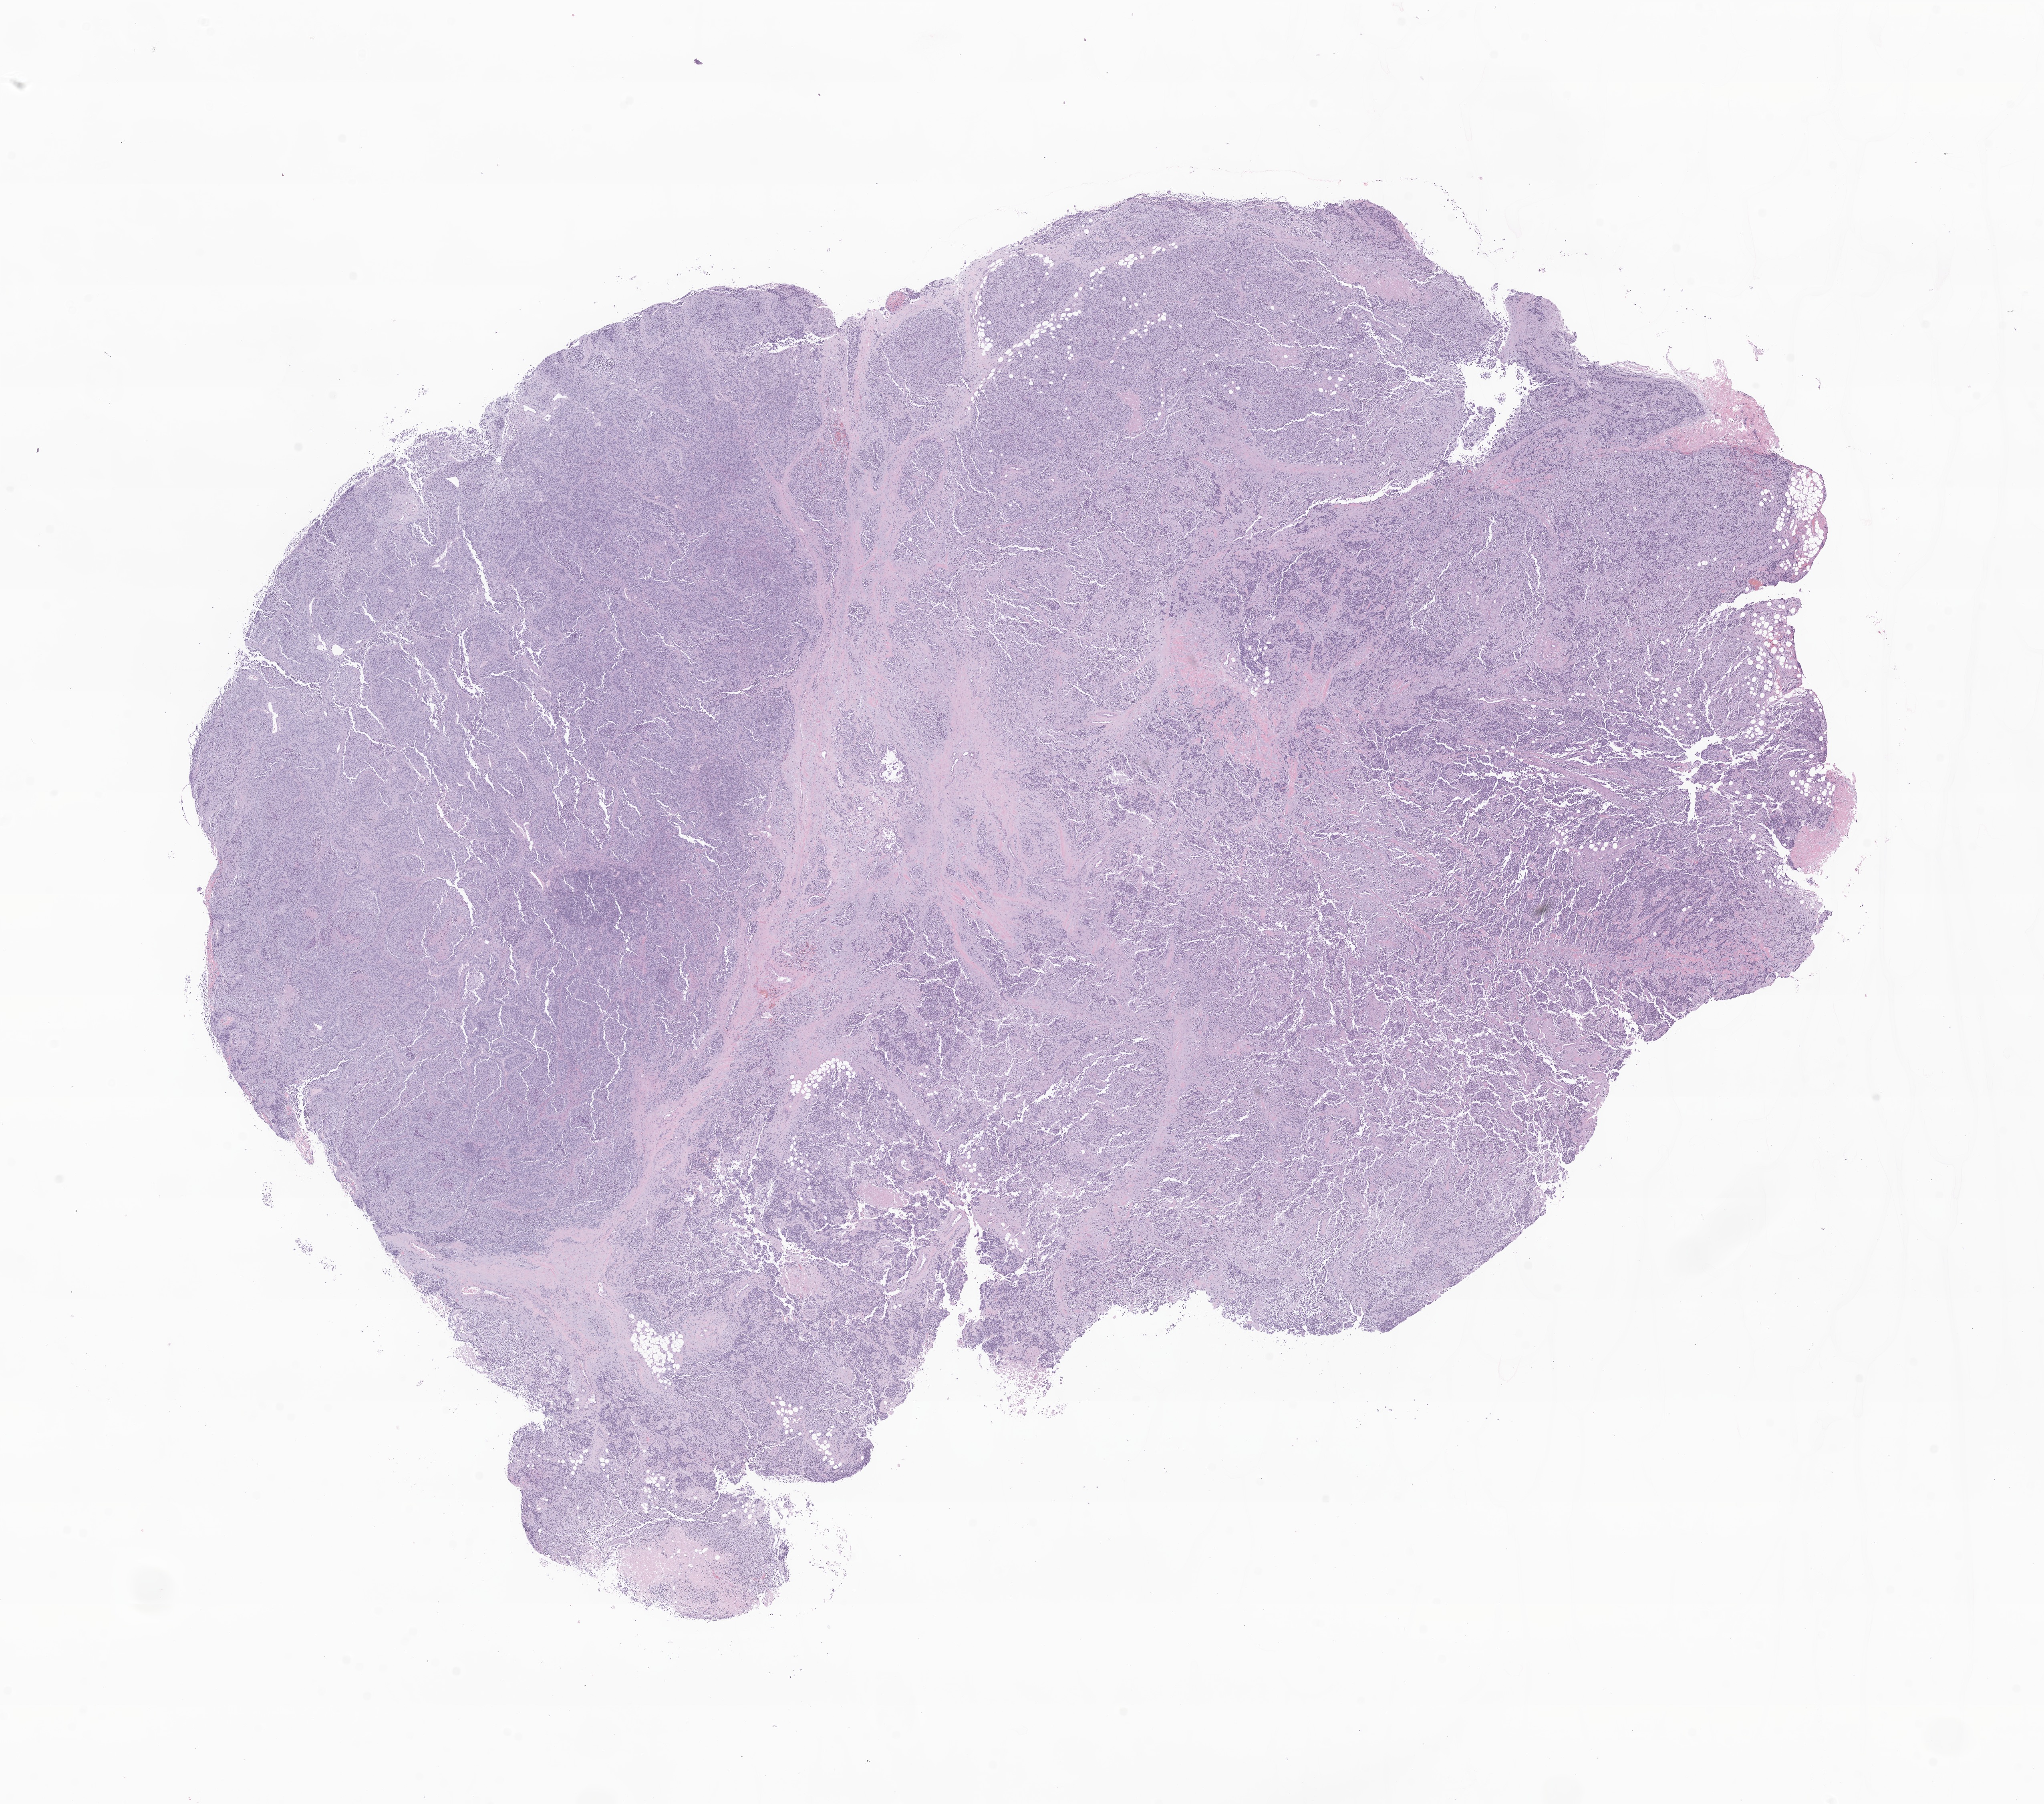
Digitized hematoxylin and eosin (H&E)-stained section of tumor tissue from the lower limb lymph node — low-resolution overview of the scanned area, about 21.5 x 19.0 mm. Formalin-fixed, paraffin-embedded (FFPE) tissue. Patient: male, age 48 months.
- recorded diagnosis: Rhabdomyosarcoma, NOS